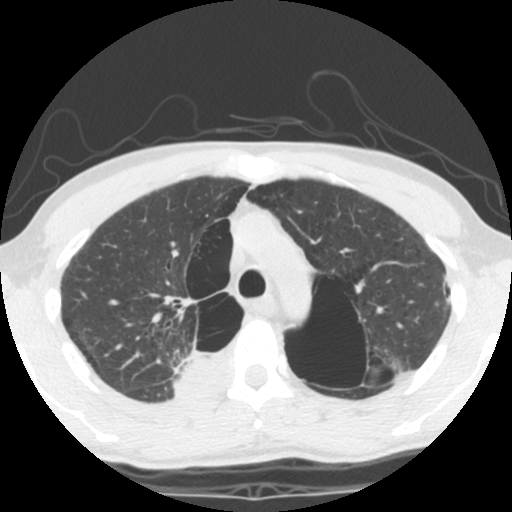
Axial slice from a low-dose chest CT screening exam, second annual screen, lung window (W 1500 / L -600 HU), 2.5 mm slice thickness, standard (soft-tissue) reconstruction kernel (STANDARD). Male participant, aged 62 years at enrolment. Current smoker at enrolment.
• Lesion marked by an expert reader, box from (x=130, y=327) to (x=230, y=408) px.
• The exam's reader record, not a measurement of the box and not confirmed to be the same lesion: non-calcified nodule or mass ≥4 mm, 35 × 25 mm, soft tissue attenuation.
• Participant outcome: lung cancer diagnosed 14 days after this screen — non-small cell carcinoma, right upper lobe, poorly differentiated (G3), stage IA (AJCC 6th edition), 70 mm at pathology.